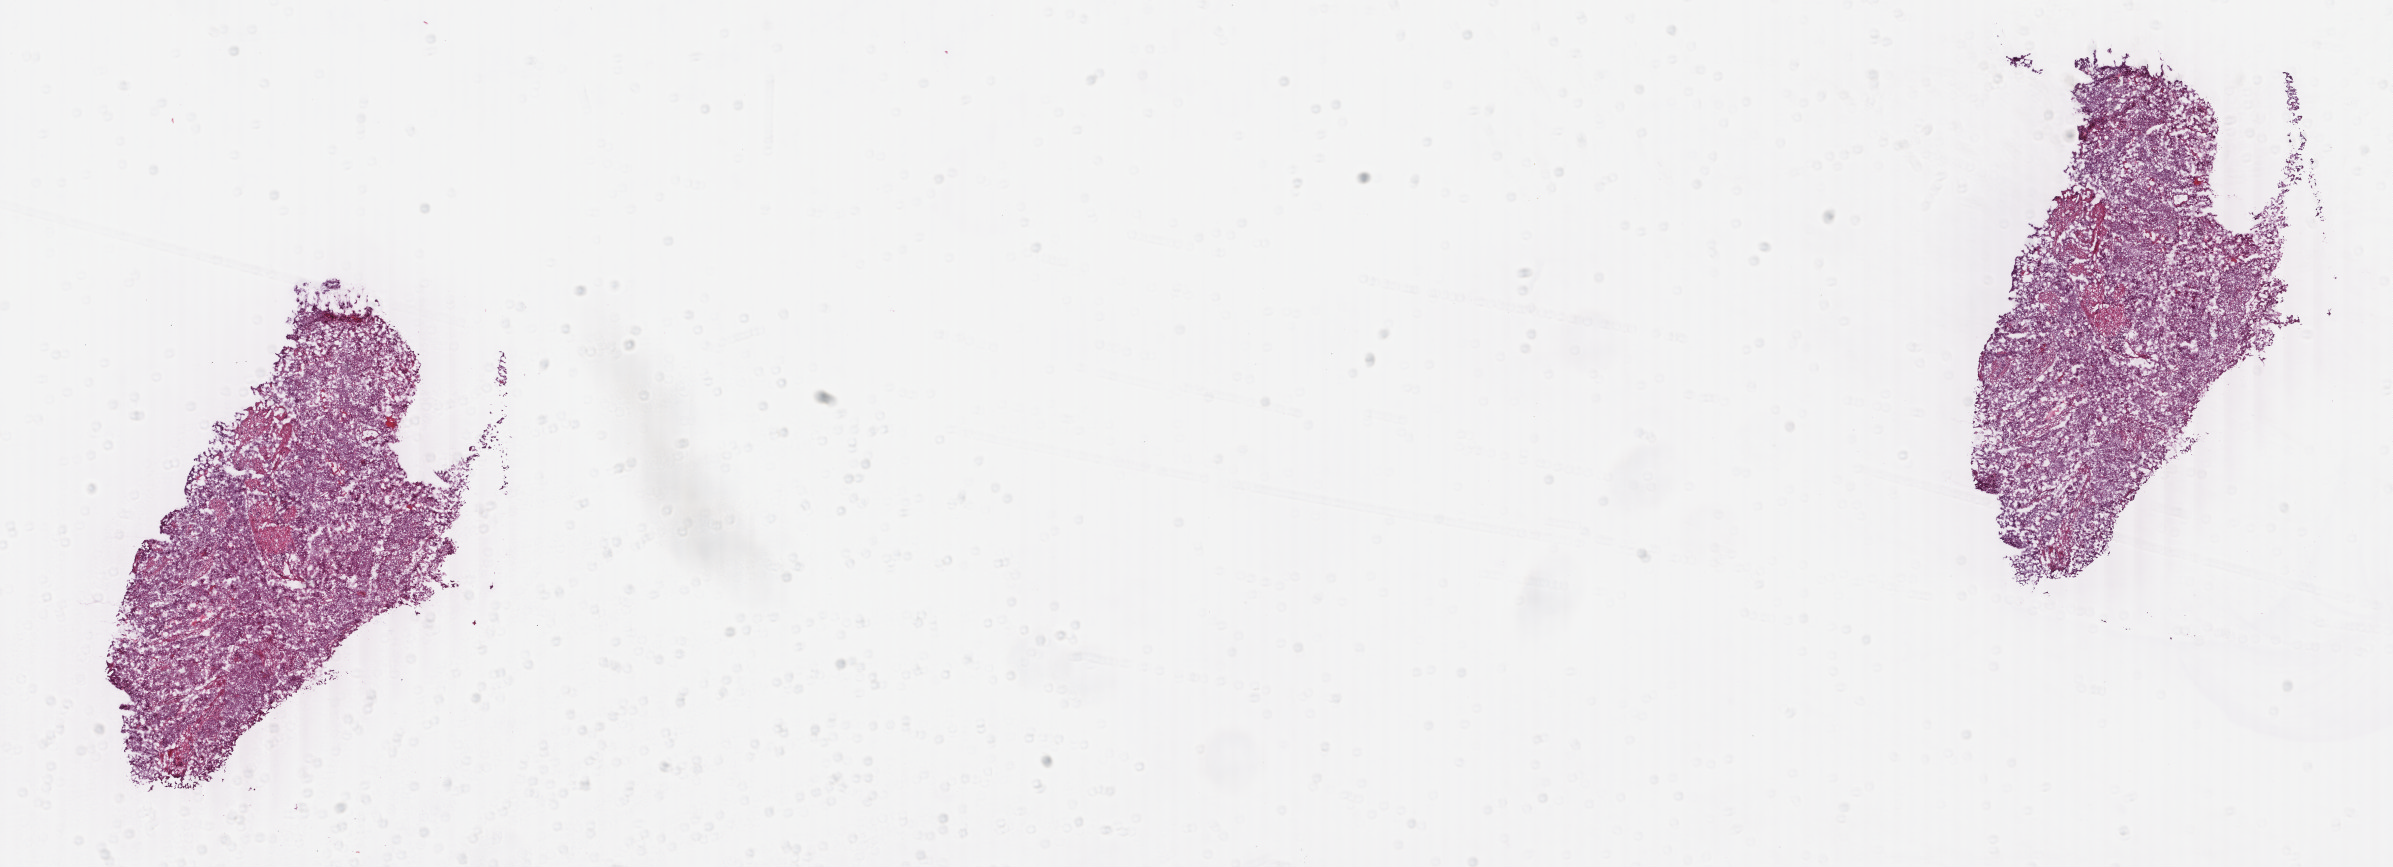
Digitized H&E-stained tissue section (whole slide) — a low-resolution overview of the entire scanned area, about 19.0 x 6.9 mm (slide scanned at 40x). Frozen section. Sample: primary tumour, uterus. Patient: female, age at initial diagnosis 72 years. Histologic grade: G3 (poorly differentiated). Pathologist review of this section (percent, as recorded): tumour cells 78%, tumour nuclei 85%, normal cells 18%, stromal cells 2%, necrosis 2%. Inflammatory infiltration, as recorded: lymphocyte infiltration 7%, monocyte infiltration 0%, neutrophil infiltration 0%.
- lymph nodes positive (case pathology): 0 of 8 examined
- FIGO stage: IIA
- diagnosis: Endometrioid adenocarcinoma, NOS (endometrium)